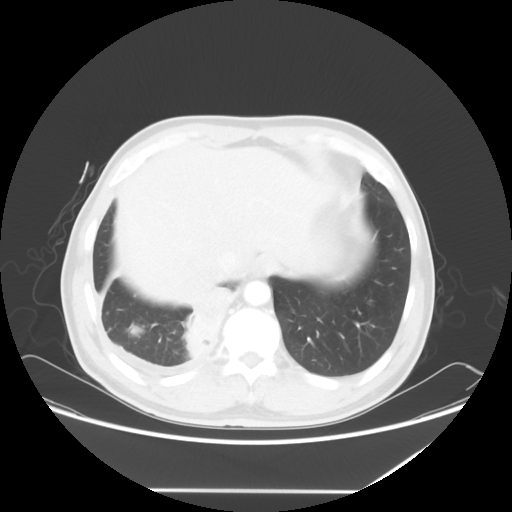
Chest CT, one axial slice; position 12 of 60 along the scan axis; 120 kVp; lung window (W 1500 / L -600 HU); 5 mm slice thickness; 512 × 512 image matrix, field of view 419 × 419 mm. Patient: male, 48 years. Case-level facts recorded for this patient, not image findings: clinical TNM (as recorded): T3 N3 M1a.
Outlined on this slice (rectangle marked by the reading radiologist):
- lung tumour (recorded histology: squamous cell carcinoma): bounding box (x1, y1, x2, y2) in pixels: (181, 282, 236, 365)